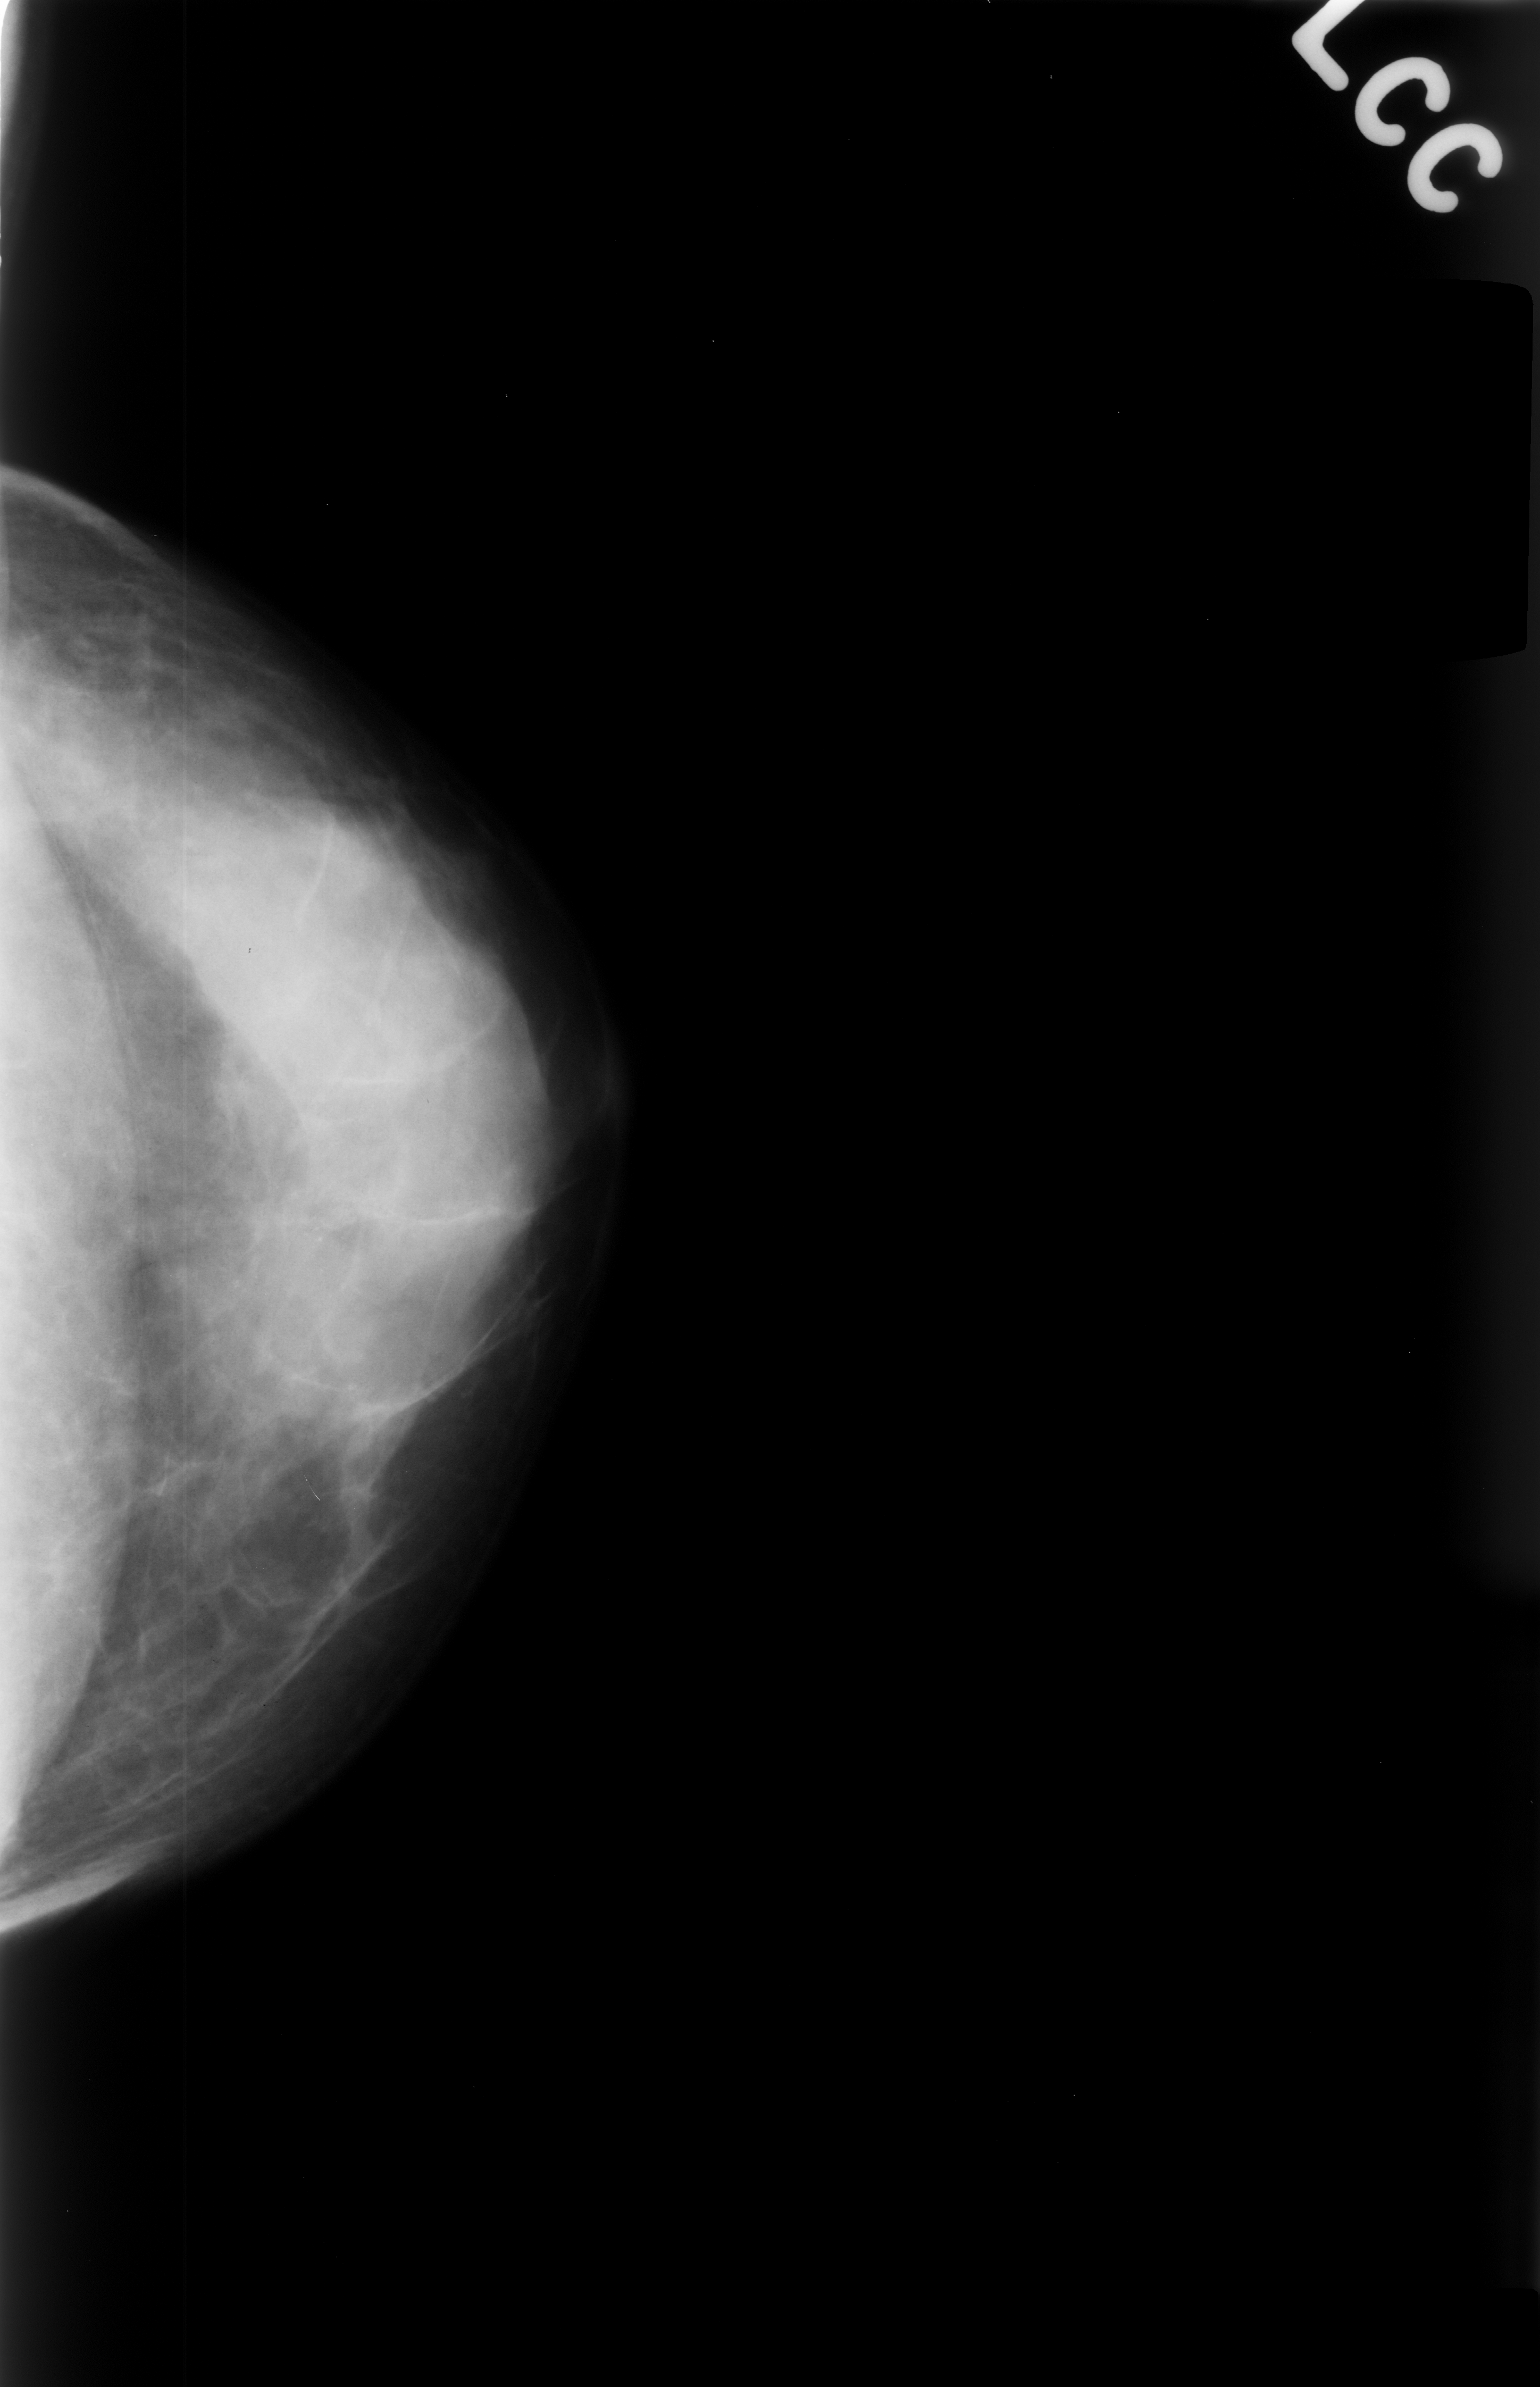
Mammogram (digitized film); left breast; CC view; breast composition: extremely dense (BI-RADS density category 4 of 4); 1540 × 2387 image matrix.
Expert-marked regions of interest on this image (one box per marked abnormality):
- calcifications, morphology punctate, distribution clustered; BI-RADS assessment category 4; subtlety rating 3 on a 1 (subtle) to 5 (obvious) scale; pathology result (as recorded, not read from the image): benign: bounding box (x1, y1, x2, y2) in pixels: (272, 1174, 448, 1329)